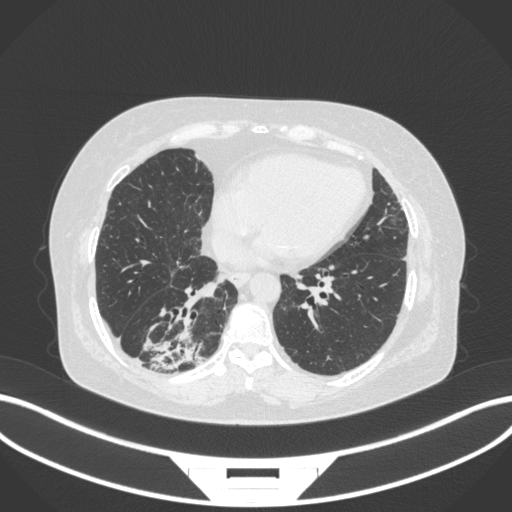
Chest CT, one axial slice; slice 78 of 303 in the series (ordered by position); reconstruction kernel B31f; 120 kVp; lung window (W 1500 / L -600 HU); 1 mm slice thickness; 512 × 512 image matrix, field of view 400 × 400 mm. Patient: female, 65 years. Case-level facts recorded for this patient, not image findings: clinical TNM (as recorded): T2b N1 M0.
Annotated regions visible in this slice (bounding box drawn by a radiologist):
- lung tumour (recorded histology: adenocarcinoma): bounding box [x1, y1, x2, y2] px = [137, 322, 206, 374]